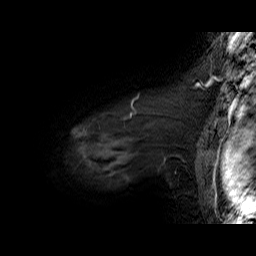
Breast MRI (dynamic contrast-enhanced), one sagittal slice. Position 56 of 60 along the scan axis. Dynamic contrast-enhanced series, time point 2 of 6 at this slice position (early post-contrast). 1.5 T. TE 6.3 ms, TR 32.9 ms. 256 × 256 image matrix, field of view 200 × 200 mm. Female patient. Case-level facts recorded for this patient, not image findings: setting: breast cancer imaged before/during neoadjuvant chemotherapy; receptor status: HER2-positive.
Outlined on this slice (semi-automatic segmentation, software-assisted and operator-edited):
- analysis volume of interest (the breast-tissue region the enhancement analysis was run in; not a lesion): box from (x=76, y=92) to (x=195, y=174) px
- tumour enhancement mask (voxels above the 100 % enhancement threshold inside the analysis volume of interest): (x=130, y=96)–(x=138, y=116)